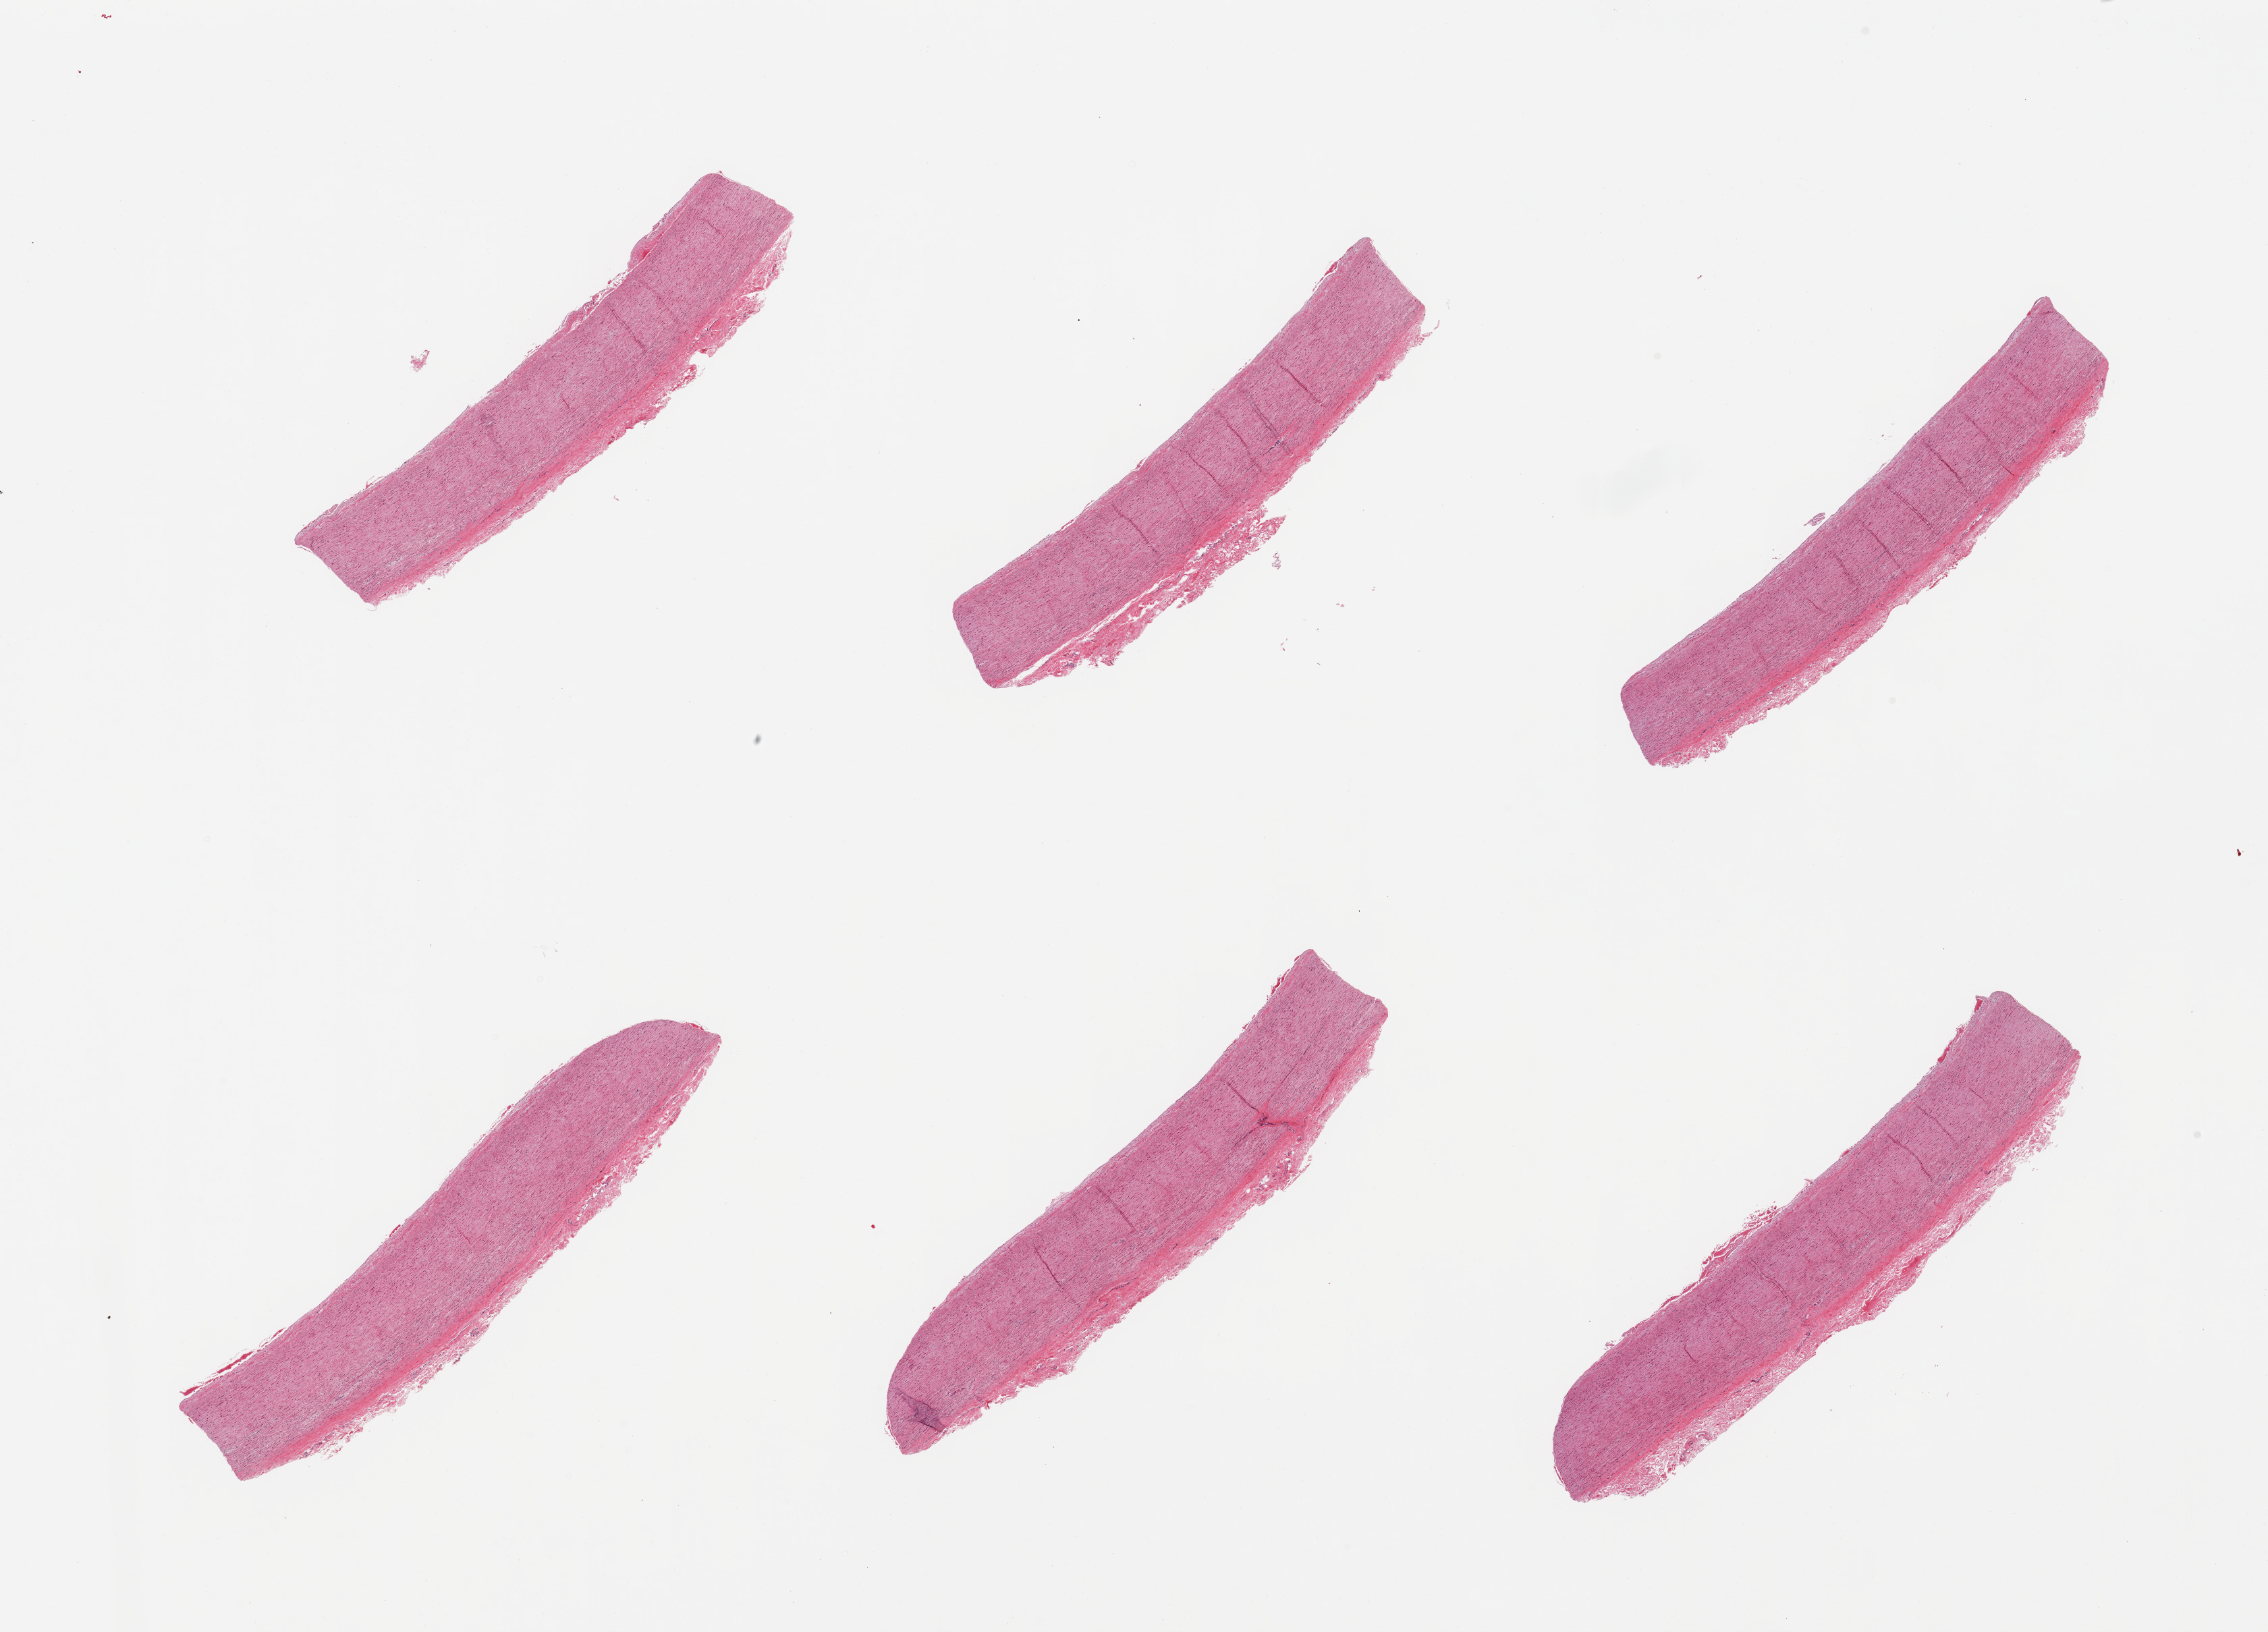
Whole-slide image, haematoxylin and eosin stain — low-resolution overview of the scanned area, about 26.6 x 19.1 mm (slide scanned at 20x); PAXgene-fixed paraffin-embedded (PFPE) section; section of aorta (target tissue); tissue donor sample. Male donor.
- pathologist's review note for this sample: 6 pieces; no plaques; well dissected